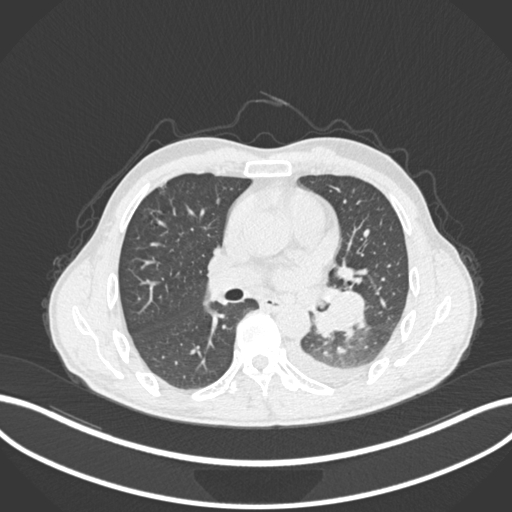
Chest CT, one axial slice. Reconstruction kernel B30f. Lung window (W 1500 / L -600 HU). 512 × 512 image matrix, field of view 400 × 400 mm. Patient: male, 47 years. From the clinical record (not read from this slice): clinical TNM (as recorded): T3 N1 M1c; histopathological grade: G3.
Outlined on this slice (rectangle marked by the reading radiologist):
- lung tumour (recorded histology: small cell carcinoma): bounding box [x1, y1, x2, y2] px = [310, 283, 370, 340]